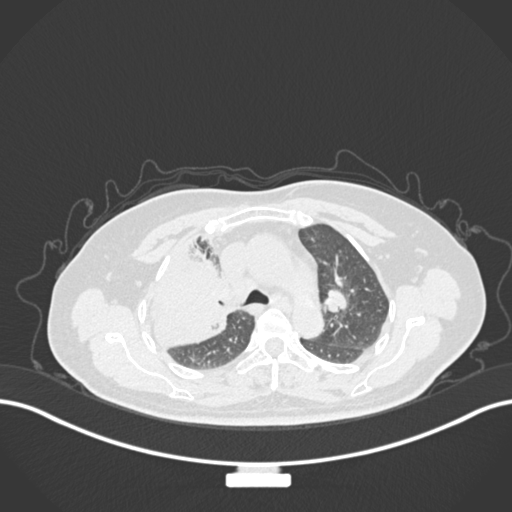
Chest CT, one axial slice; position 108 of 177 along the scan axis; reconstruction kernel B30f; lung window (W 1500 / L -600 HU); 1 mm slice thickness; 512 × 512 image matrix, field of view 400 × 400 mm. Female patient, age 60 years. Case-level facts recorded for this patient, not image findings: clinical TNM (as recorded): T3 N1 M1.
Annotated regions visible in this slice (rectangle marked by the reading radiologist):
- lung tumour (recorded histology: adenocarcinoma): box from (x=142, y=242) to (x=234, y=356) px